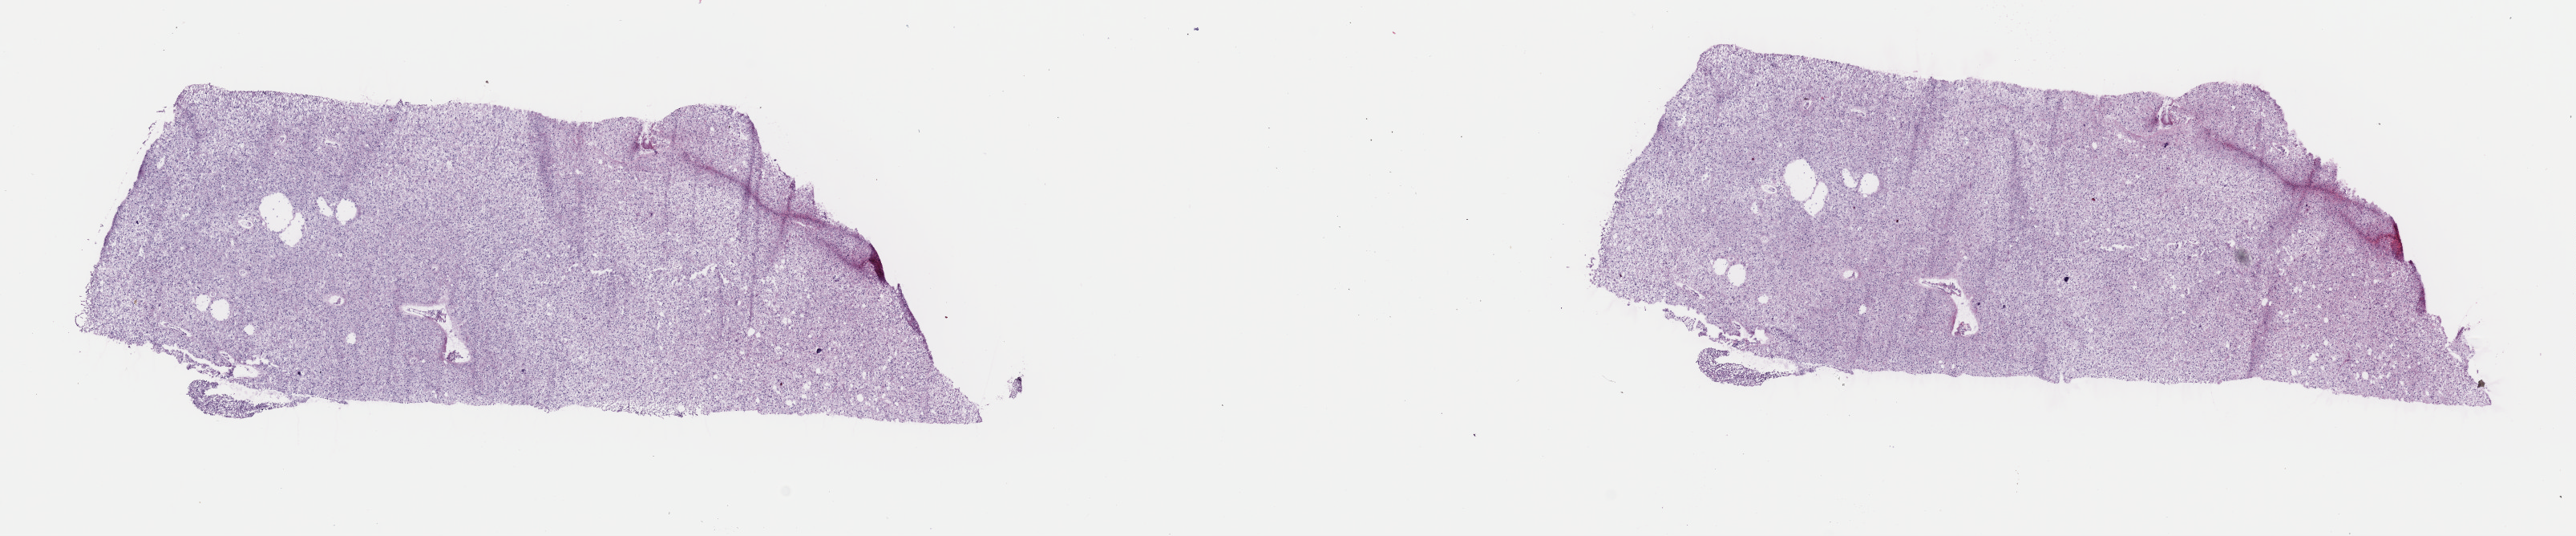
Digitized Hematoxylin and eosin (H&E) stained tissue section (whole slide), a low-resolution overview of the entire scanned area, about 25.4 x 5.3 mm (acquisition: 40x scan), frozen section from the top of the tissue portion, sample: primary tumour, brain. Male, age 34 years at initial diagnosis. Histologic grade: G2 (moderately differentiated). Pathologist review of this section (percent, as recorded): tumour cells 70%, tumour nuclei 90%, normal cells 10%, stromal cells 20%, necrosis 0%. Inflammatory infiltration, as recorded: lymphocyte infiltration 0%, monocyte infiltration 0%, neutrophil infiltration 0%.
• pathologic diagnosis: Oligodendroglioma, NOS (cerebrum)